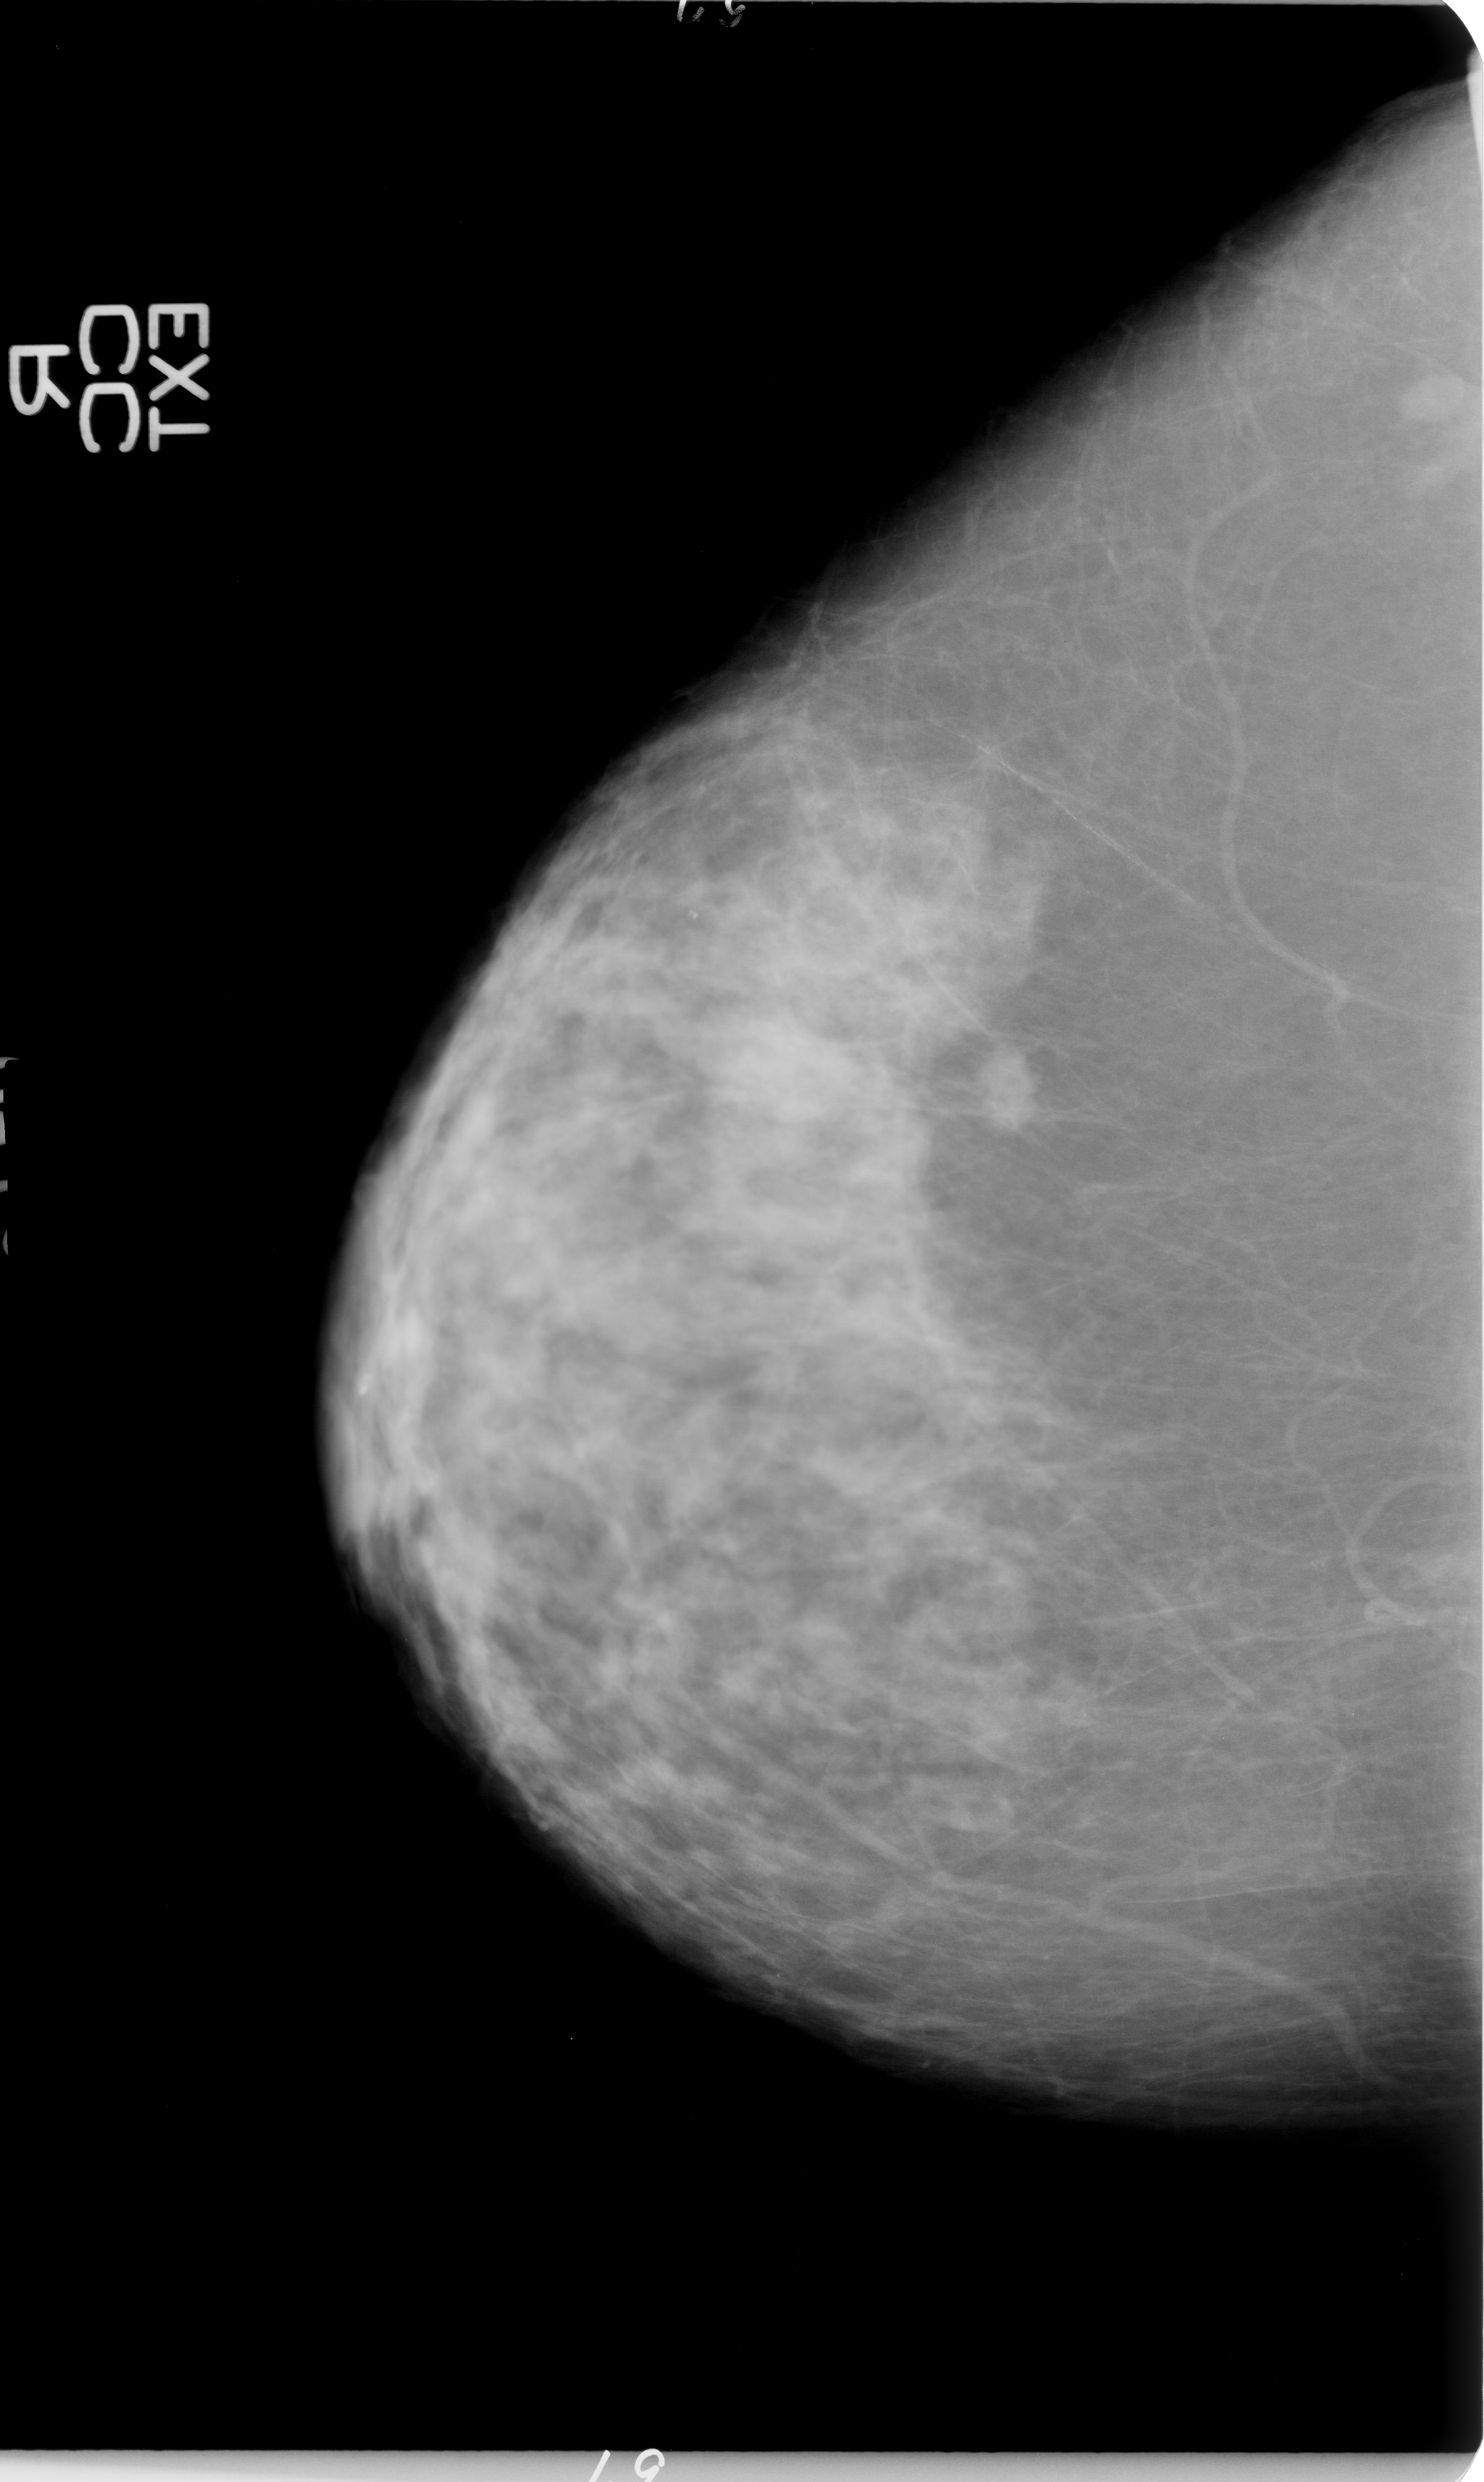
Scanned film-screen mammogram. Right breast. Craniocaudal (CC) view. BI-RADS breast density category 3 (scale 1–4). 1484 × 2482 image matrix.
Expert-marked regions of interest on this film, with their recorded descriptors:
- mass, shape irregular, margins microlobulated; BI-RADS assessment category 4; pathology (as recorded): malignant: bounding box <952,1030,1058,1147> (left, top, right, bottom; pixels)